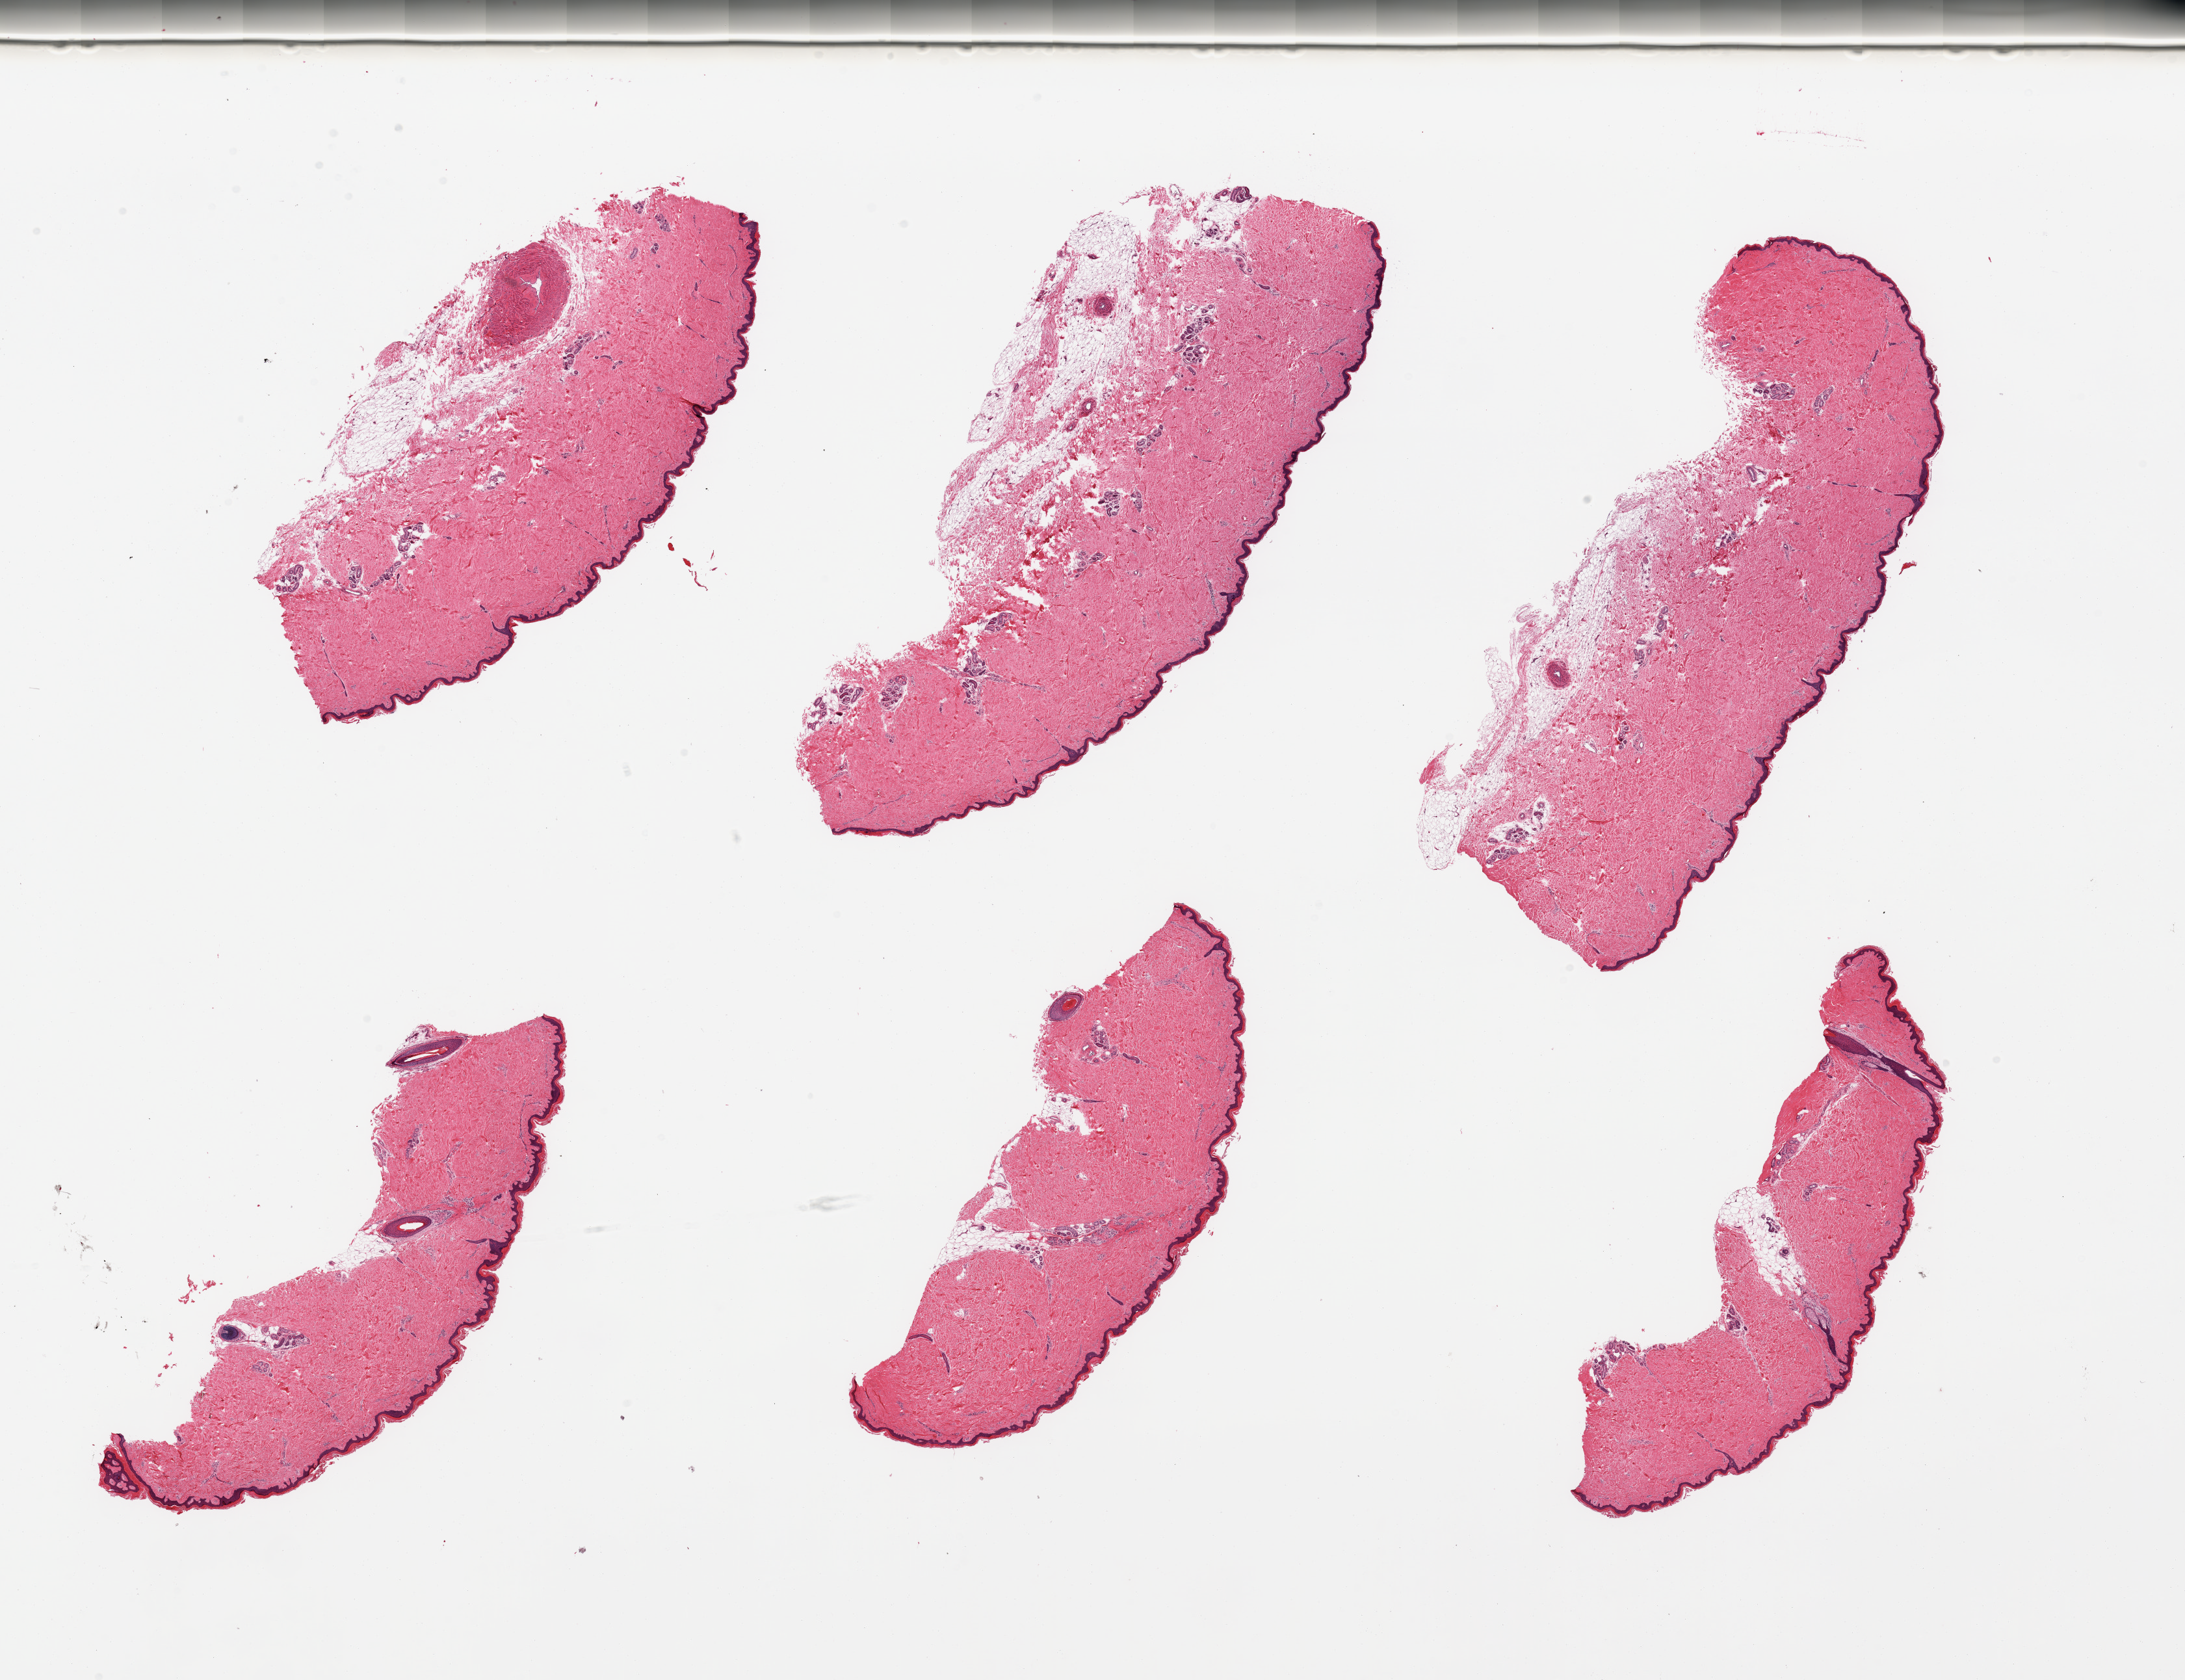
Whole-slide image, haematoxylin and eosin stain, brightfield, shown as a low-resolution overview of the whole scanned area (about 26.6 x 20.4 mm, acquisition: 20x scan); PAXgene-fixed paraffin-embedded (PFPE) section; target tissue: skin of lower leg; tissue donor sample.
- review note (as recorded): 6 pieces; 3 with subcutaneous fat and 1 0.9mm artery; up to 10% dermal fat